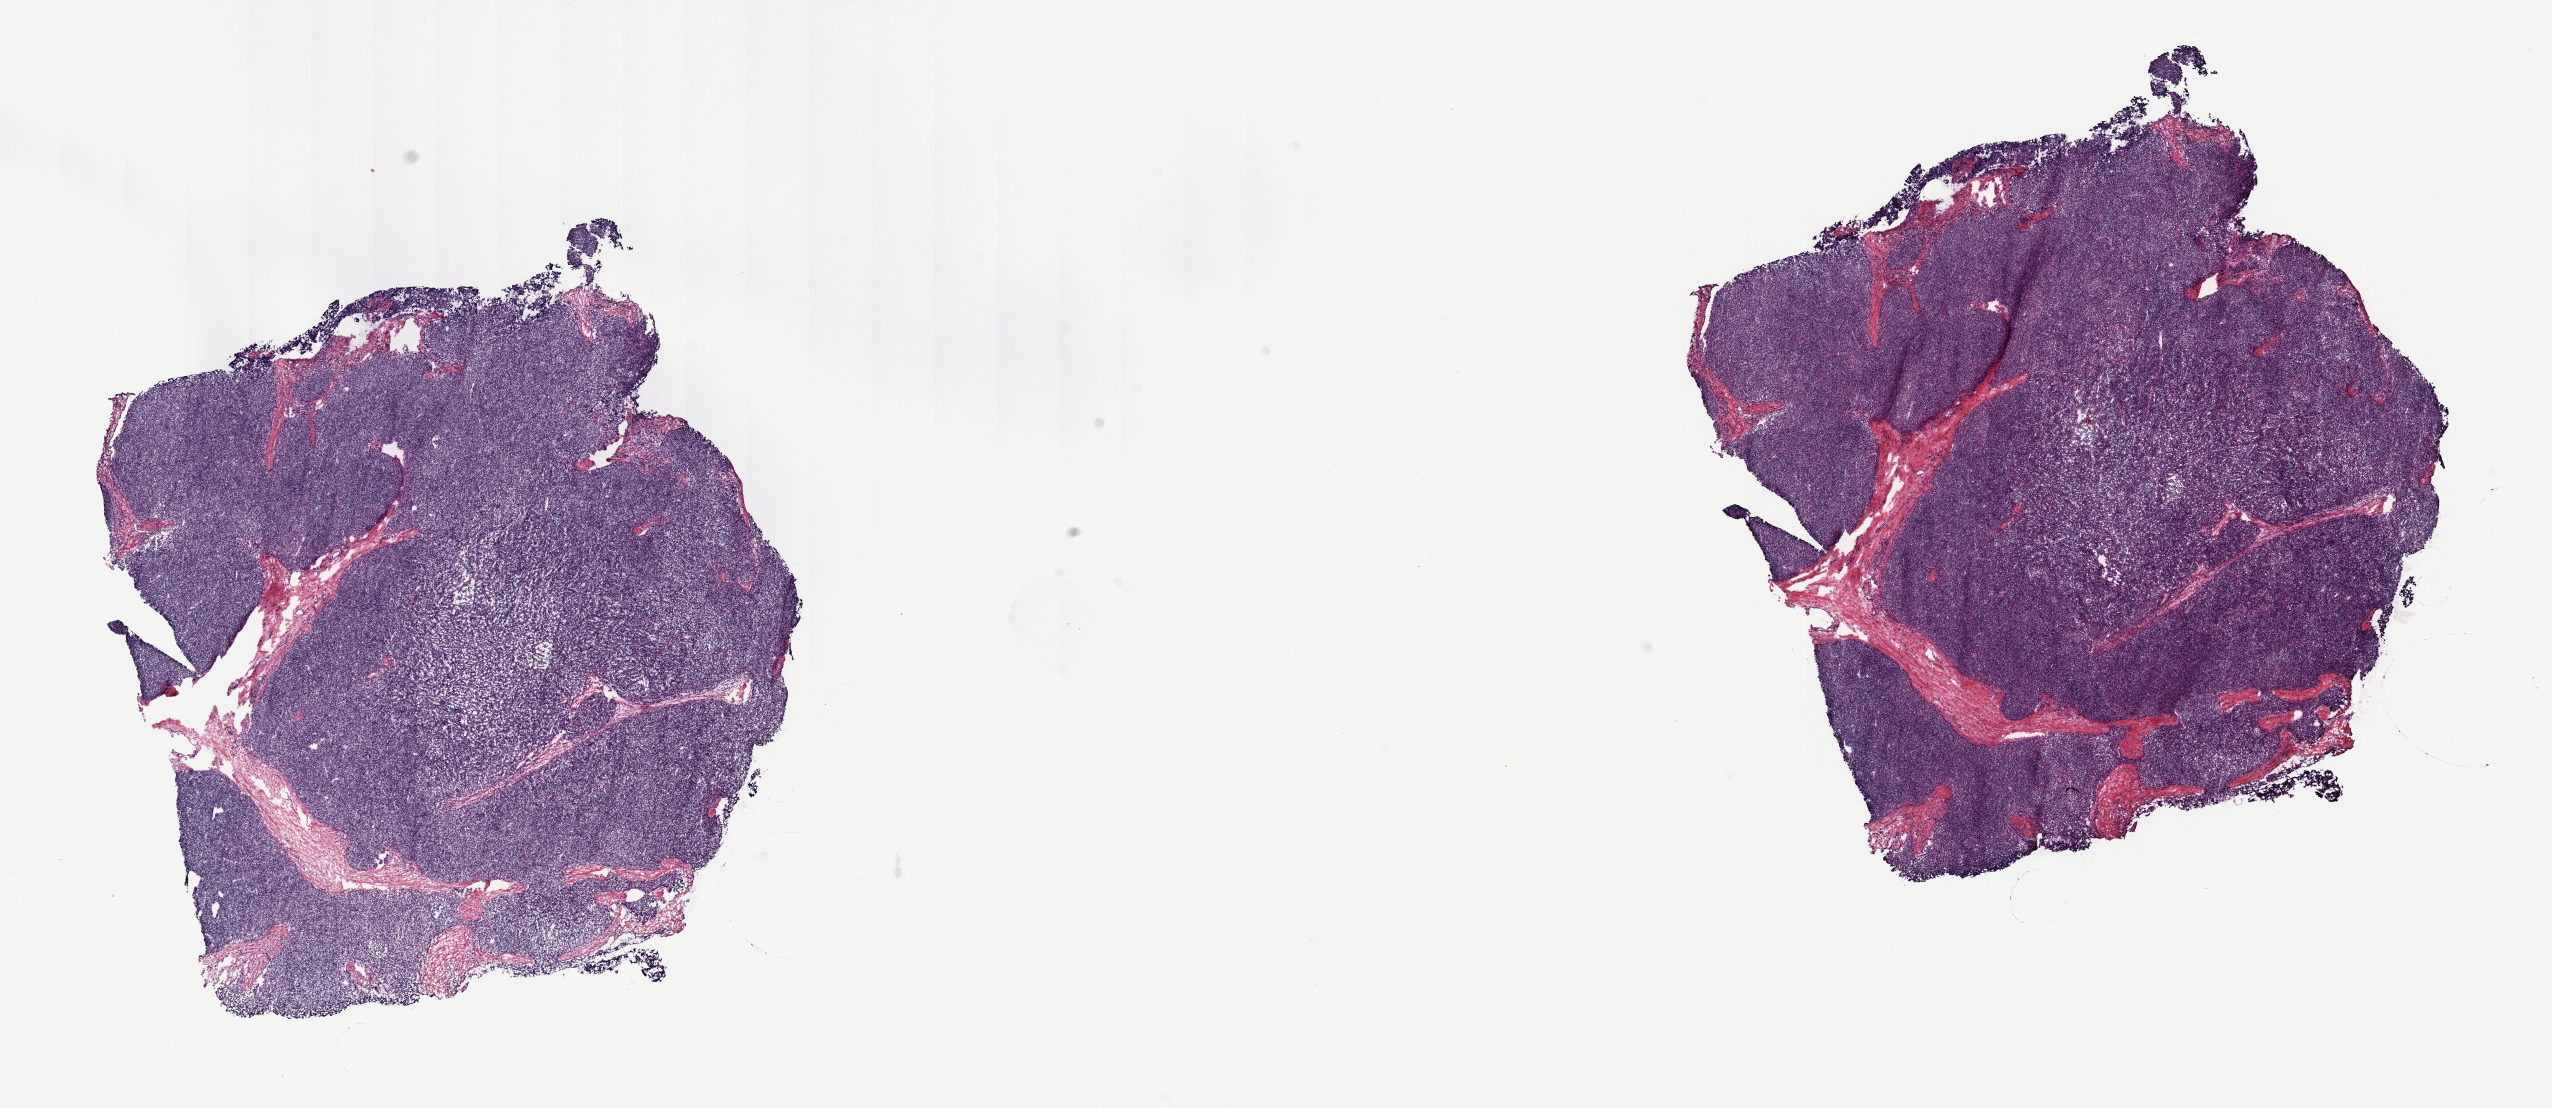
Whole-slide histology image, H&E — low-resolution overview of the scanned area, about 20.6 x 9.0 mm; frozen section from the top of the tissue portion; primary tumour sample from the thymus. Male patient; age at initial diagnosis 43 years. Pathologist review of this section (percent, as recorded): tumour cells 85%, tumour nuclei 85%, normal cells 0%, stromal cells 15%, necrosis 0%. Infiltration values recorded for this section: lymphocyte infiltration 3%, monocyte infiltration 1%, neutrophil infiltration 1%.
• histologic diagnosis: Thymoma, type B2, malignant